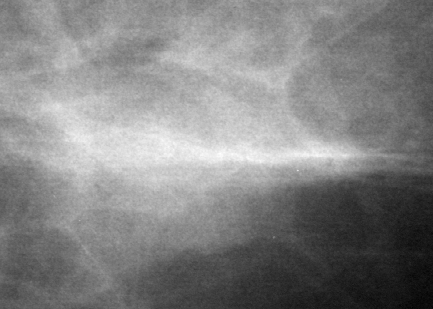
Crop from a digitized film mammogram around one marked abnormality; left breast; MLO view; BI-RADS breast density category 2 (scale 1–4).
- Marked abnormality: mass, shape oval, margins ill defined; BI-RADS assessment category 4; subtlety rating 4 on a 1 (subtle) to 5 (obvious) scale; pathology result (as recorded, not read from the image): benign.